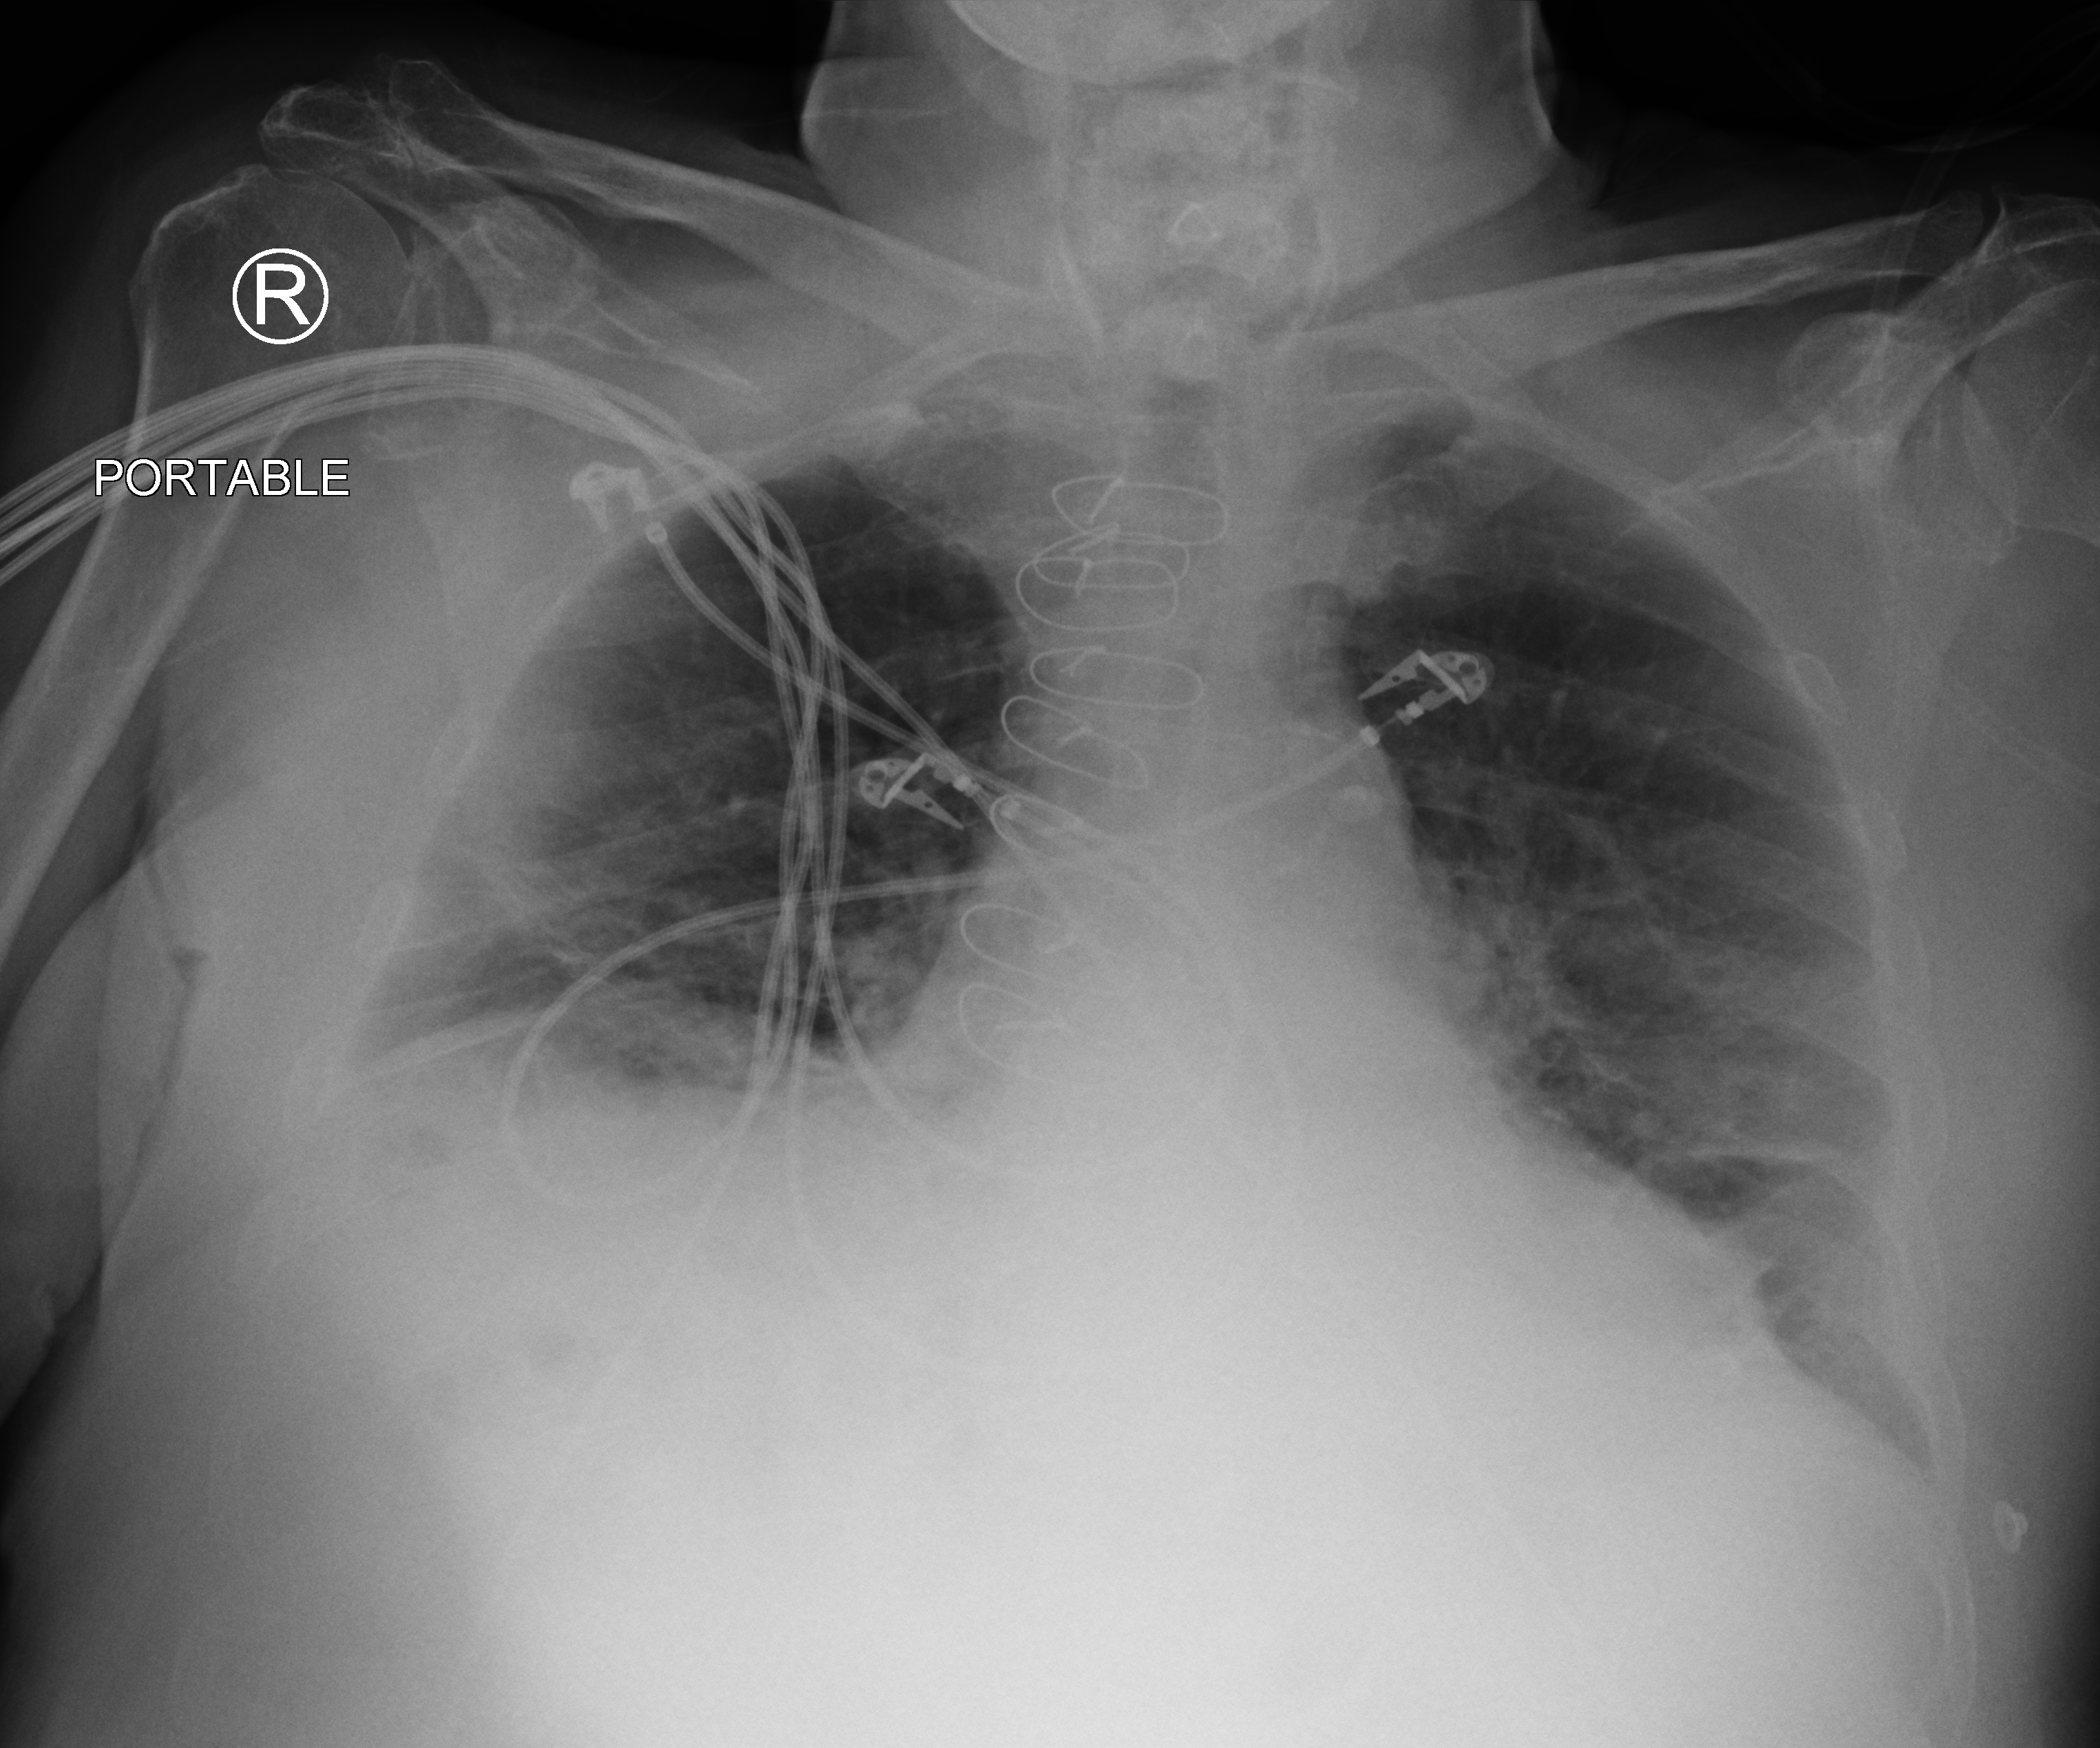
Chest X-ray (portable), anteroposterior (AP) projection. Patient hospitalised with COVID-19; male, aged 75–90 years.
Hospital-stay facts (about this admission, not read from this image; timing relative to this image not recorded):
- hypertension (admission record): yes